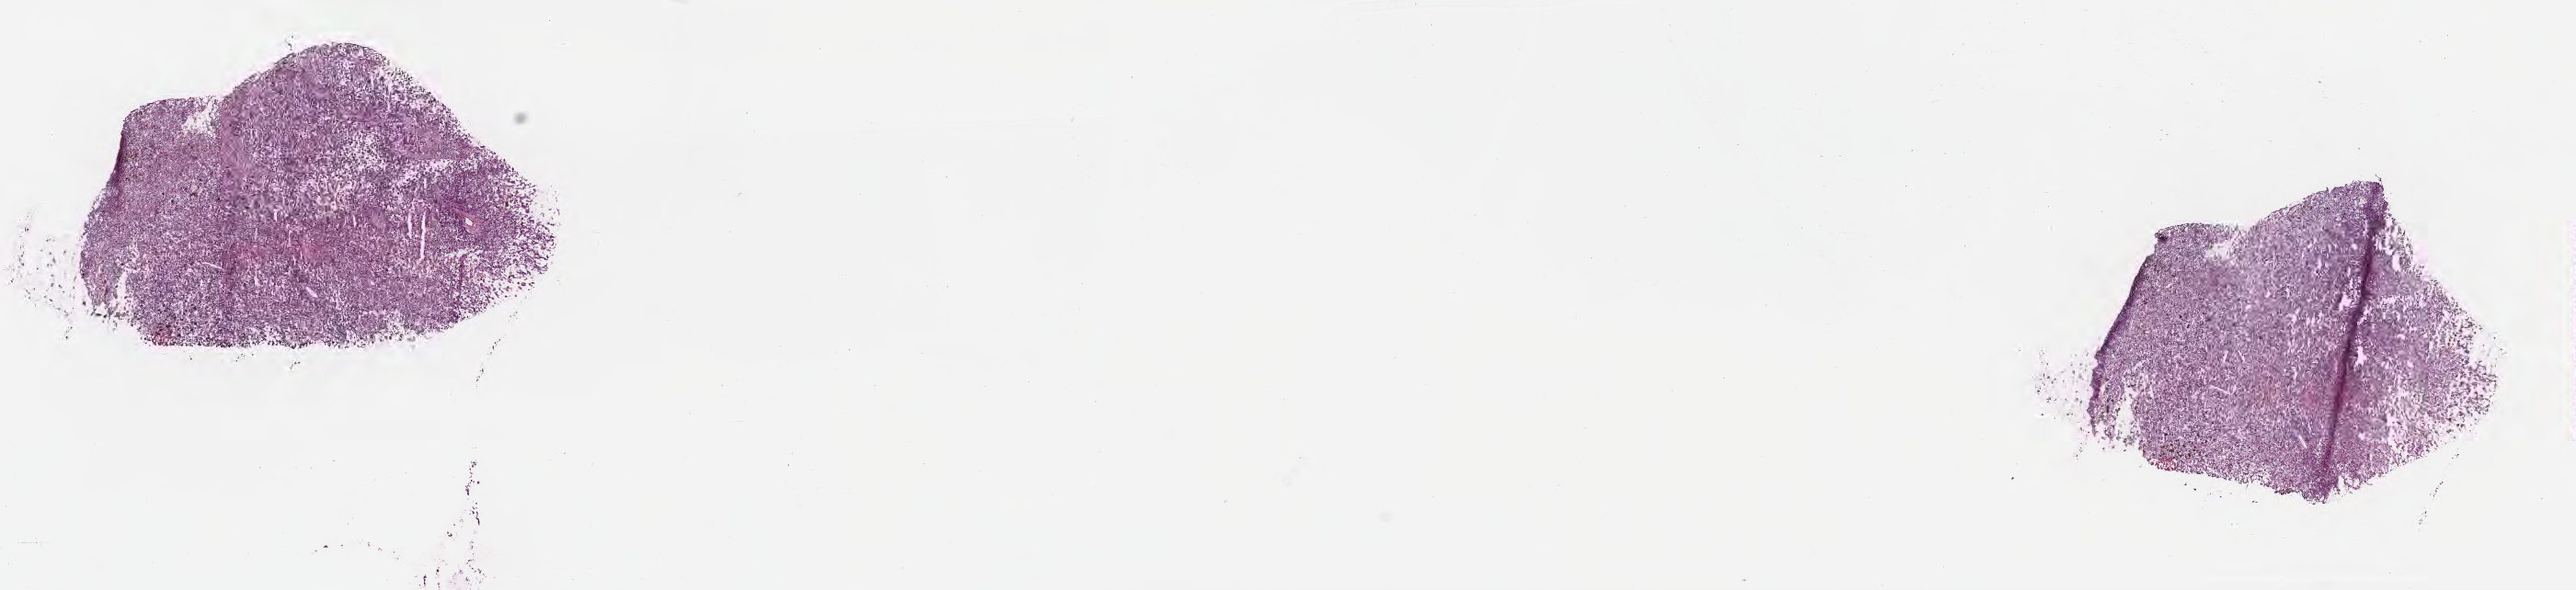
Whole-slide image, haematoxylin and eosin stain — a low-resolution overview of the entire scanned area, about 22.7 x 5.2 mm, frozen section, metastatic tumor tissue, resected from lymph node. Patient: male, age at initial diagnosis 74 years. Composition of this section per pathologist review: tumor cells 75%, tumor nuclei 78%, stromal cells 3%, necrosis 1%, normal cells 21%. Inflammatory infiltration, as recorded: lymphocyte infiltration 6%, monocyte infiltration 11%, neutrophil infiltration 0%.
Patient diagnosis (primary): Malignant melanoma, NOS. Section: bottom of the tissue portion.